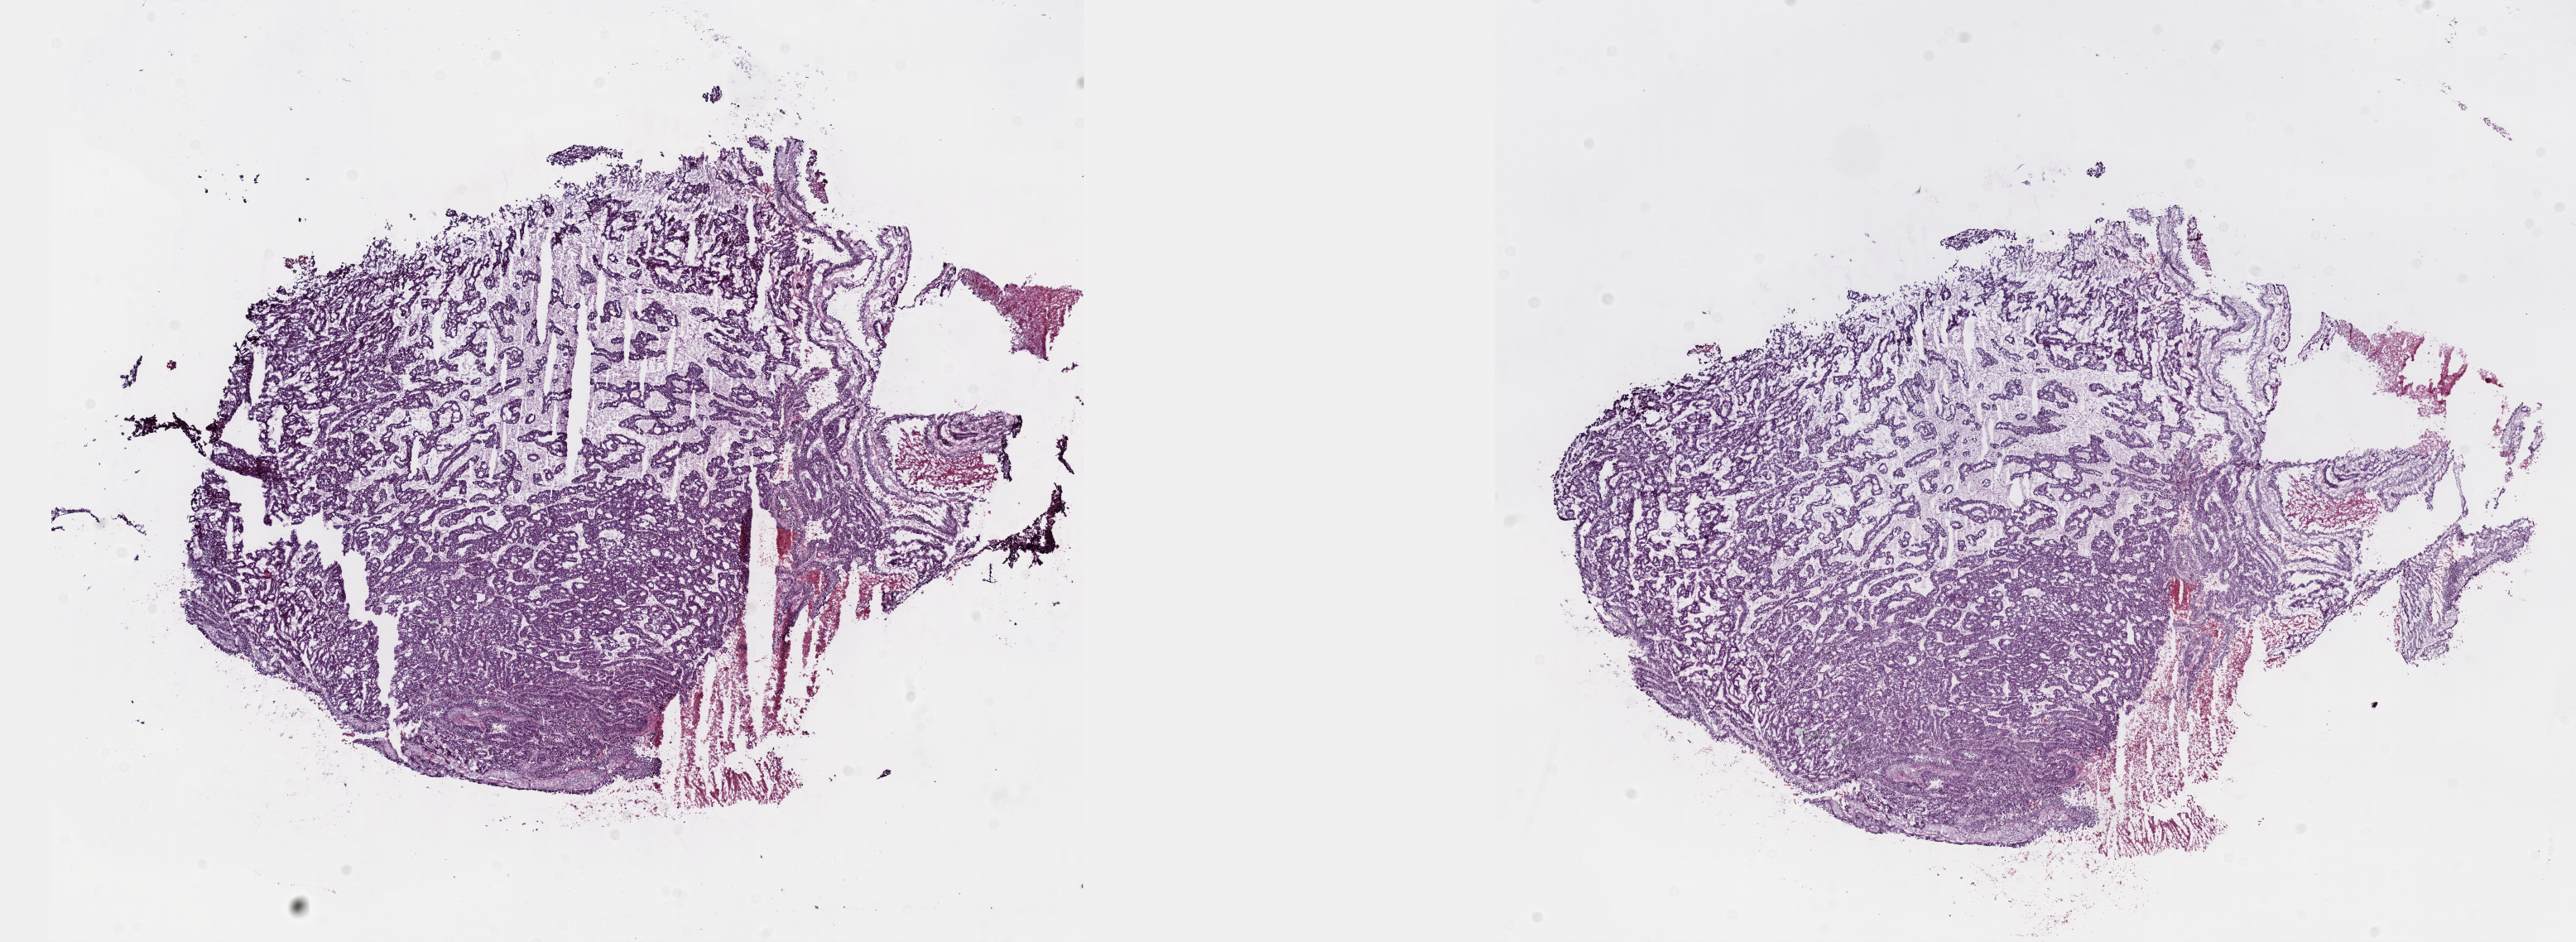
Hematoxylin and eosin (H&E) stained whole-slide image — low-resolution overview of the scanned area, about 25.1 x 9.2 mm, frozen section from the top of the tissue portion, sample: primary tumour, kidney. Male patient; age at initial diagnosis 79 years. Slide review estimates, as recorded: tumour cells 75%, tumour nuclei 75%, normal cells 0%, stromal cells 20%, necrosis 5%. Infiltration values recorded for this section: lymphocyte infiltration 2%, monocyte infiltration 5%, neutrophil infiltration 1%.
AJCC pathologic stage: I (7th edition). Laterality: left. Pathologic diagnosis: Papillary adenocarcinoma, NOS.